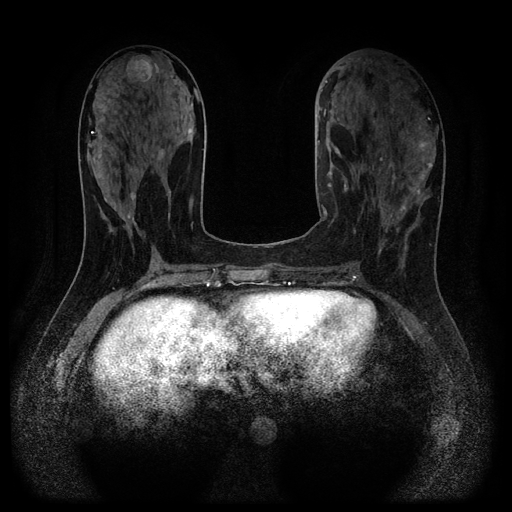
Breast MRI (dynamic contrast-enhanced, multi-phase), one axial slice. Slice 46 of 116 in the series (ordered by position). Dynamic contrast-enhanced series, time point 2 of 5 at this slice position (early post-contrast). 1.5 T. TE 2.7 ms, TR 5.4 ms. 2.2 mm slice thickness. 512 × 512 image matrix, field of view 330 × 330 mm. Patient: female, 43 years.
Outlined on this slice (semi-automatic segmentation, software-assisted and operator-edited):
- breast lesion (labelled benign in the annotation): bounding box <152,146,166,161> (left, top, right, bottom; pixels)
- breast lesion (labelled benign in the annotation): <124,55,156,83>